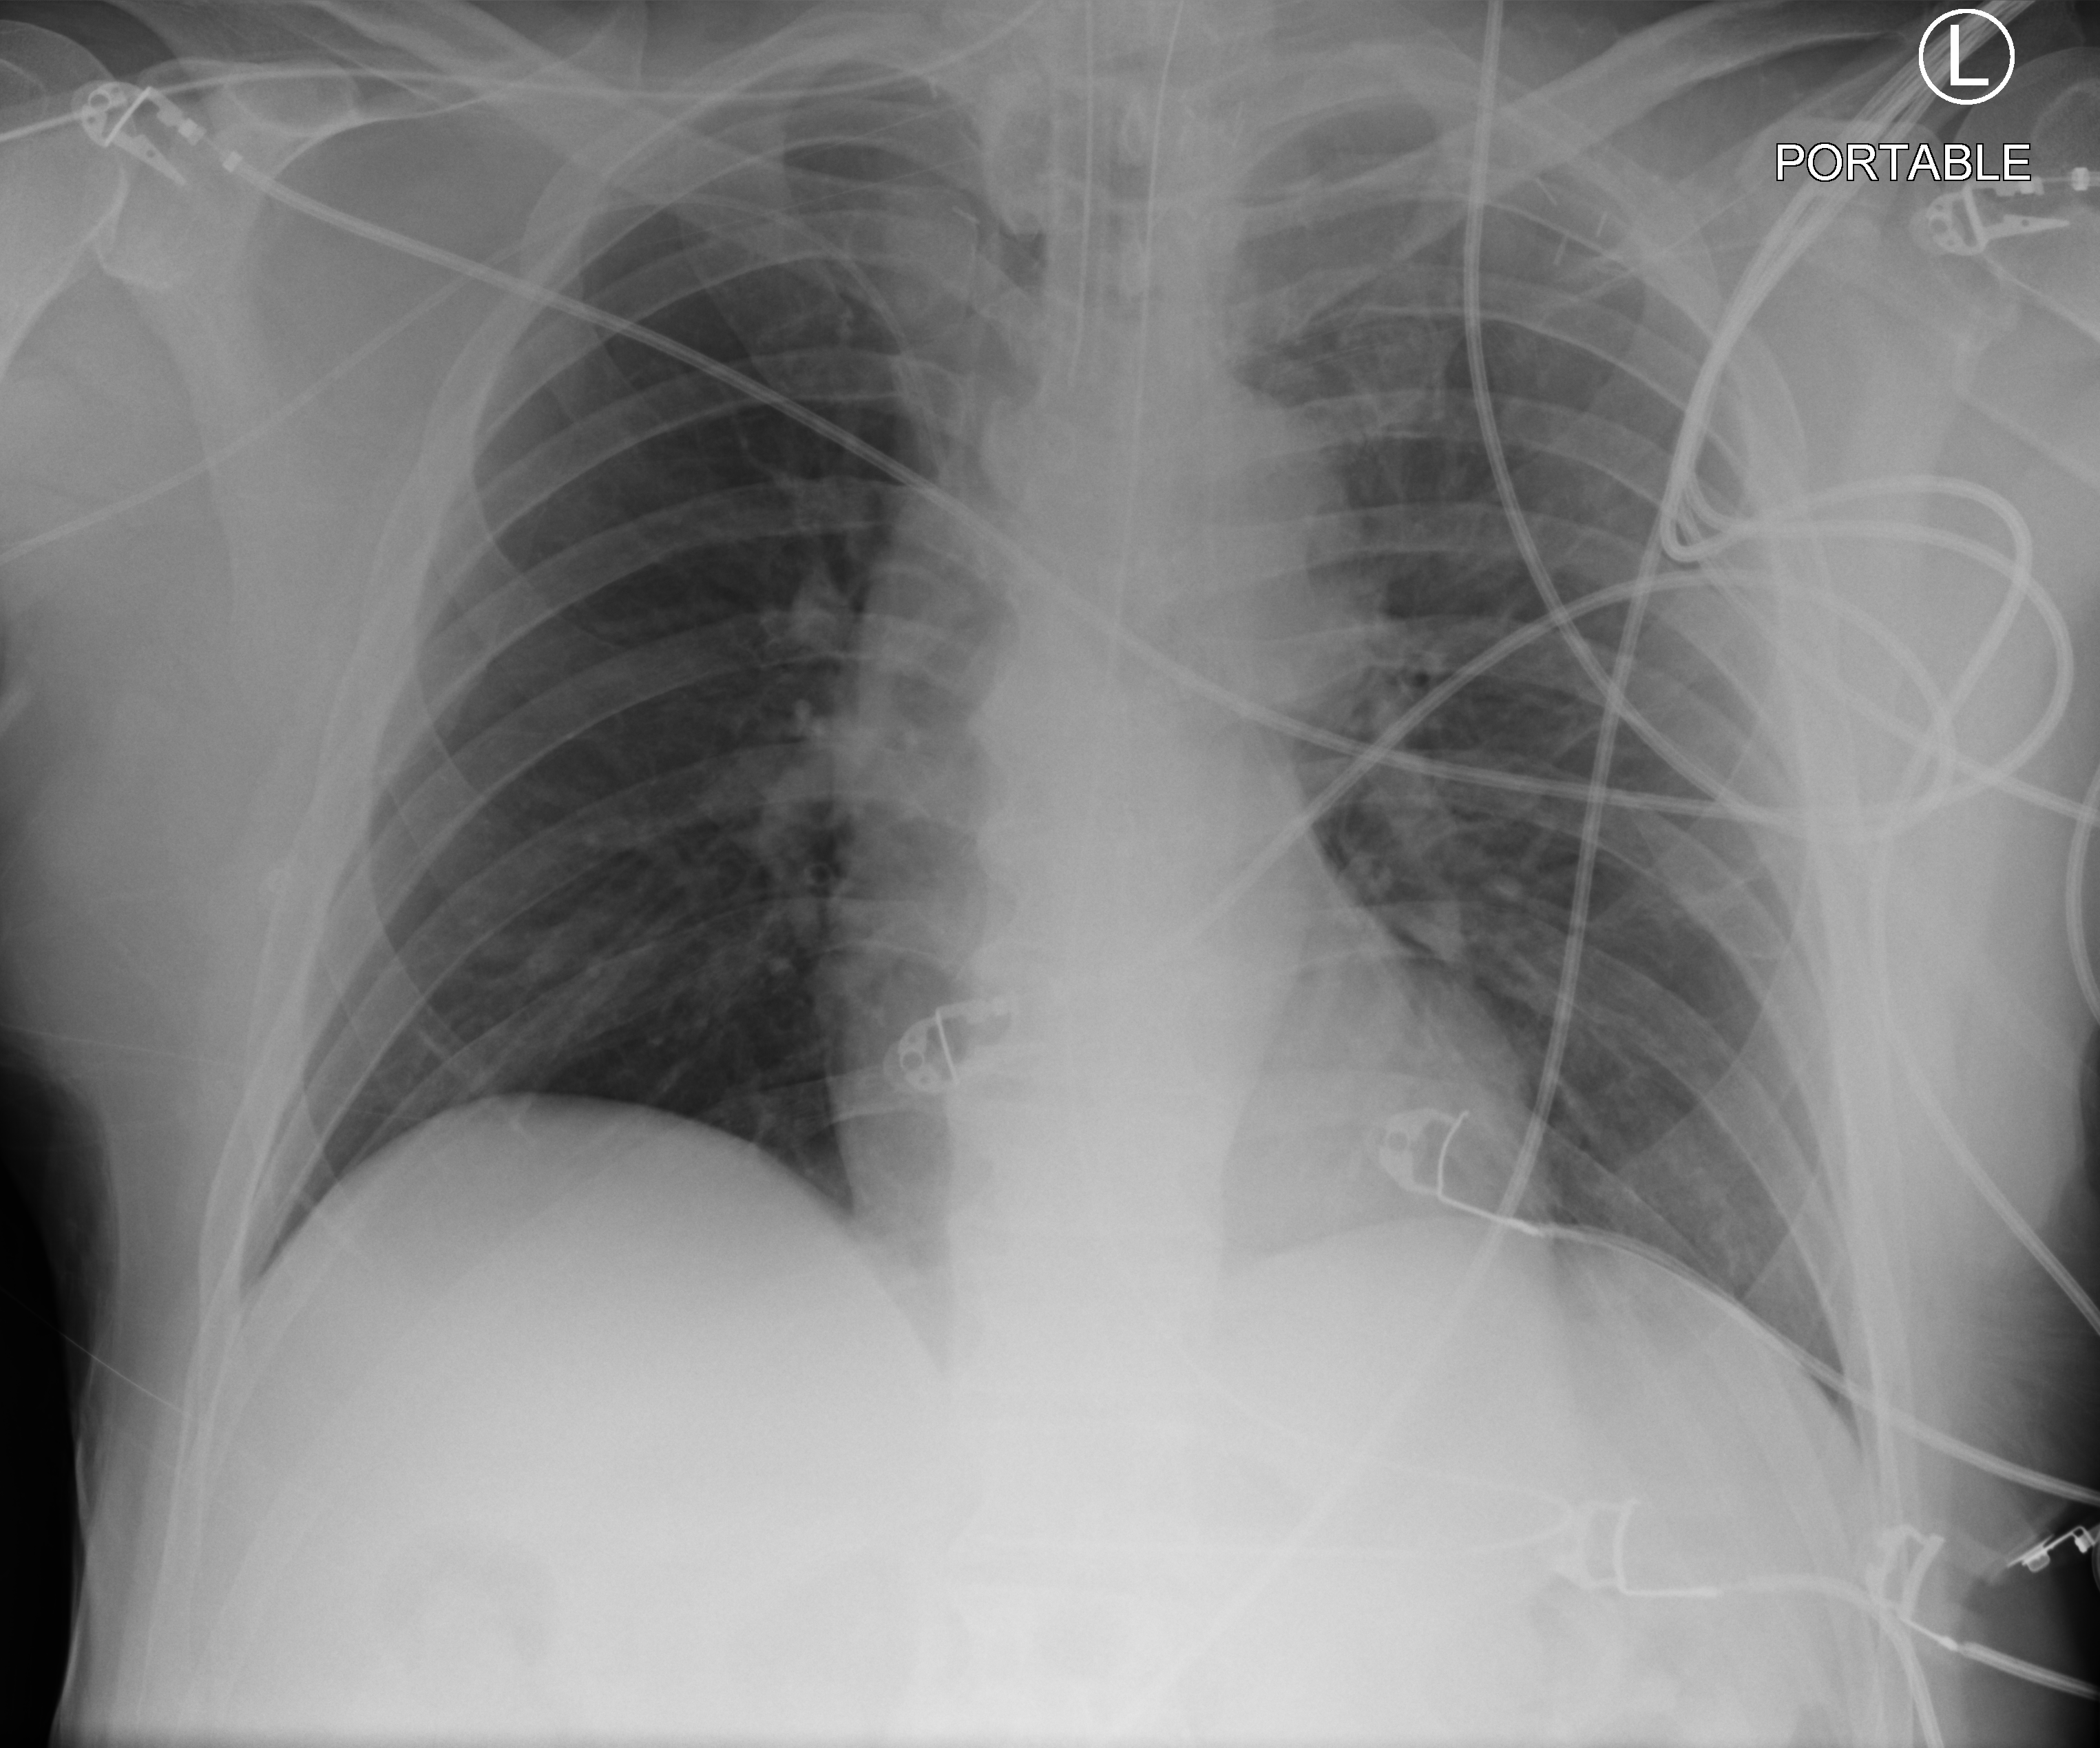
Bedside chest radiograph (computed radiography), anteroposterior (AP) projection. Patient hospitalised with COVID-19, aged 18–59 years.
Hospital-stay facts (about this admission, not read from this image; timing relative to this image not recorded): length of hospital stay: 19 days; admitted to intensive care during this hospital stay: yes.